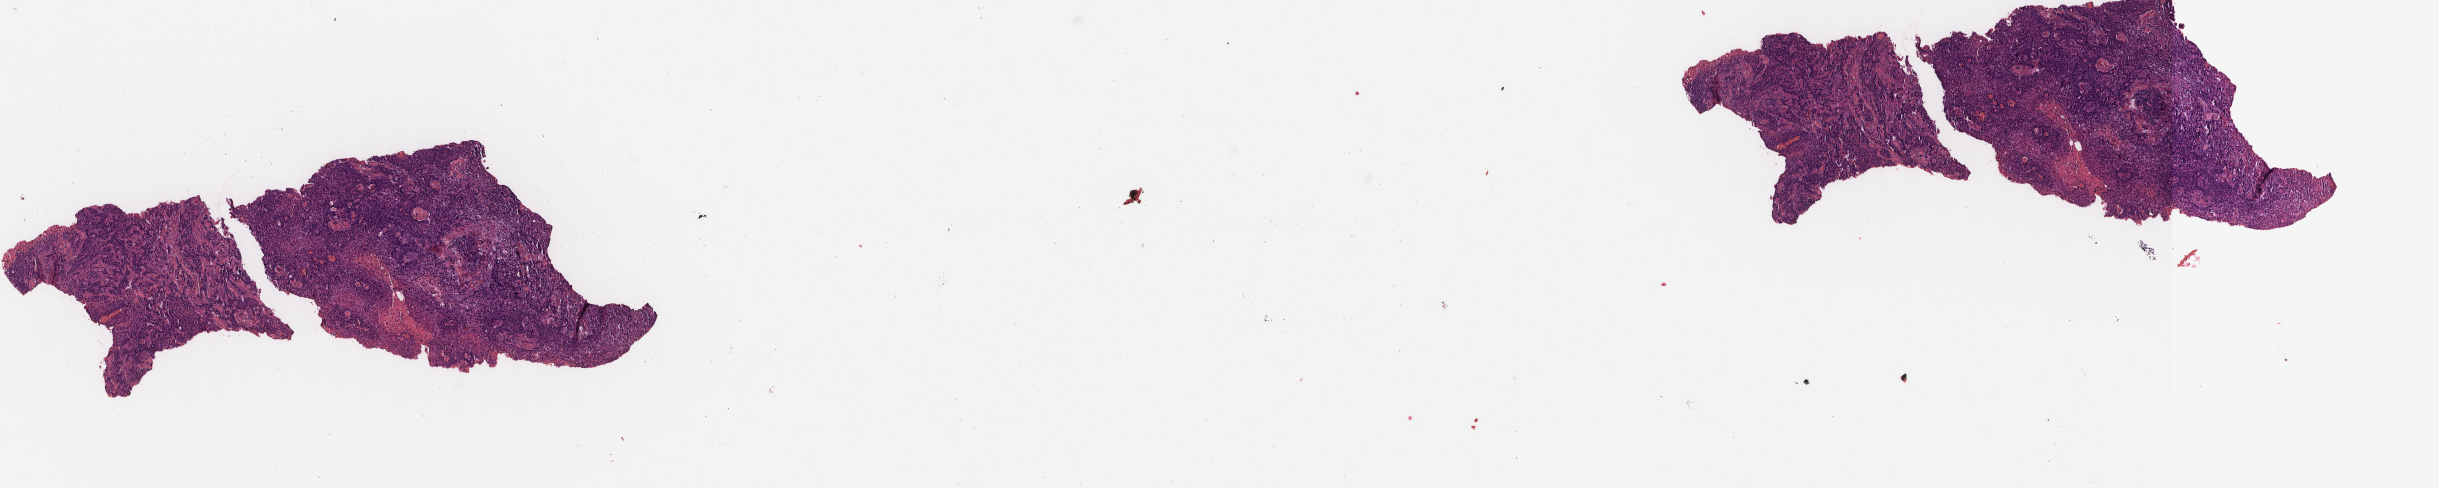
Digitized H&E-stained tissue section (whole slide) — whole scanned area (about 19.4 x 3.9 mm, acquisition: 40x scan) shown as a low-resolution overview. Formalin-fixed paraffin-embedded (FFPE) diagnostic section. Cervix, primary tumour sample. Patient: female, age at initial diagnosis 48 years. Histologic grade: G3 (poorly differentiated).
Diagnosis: Squamous cell carcinoma, NOS (cervix uteri).